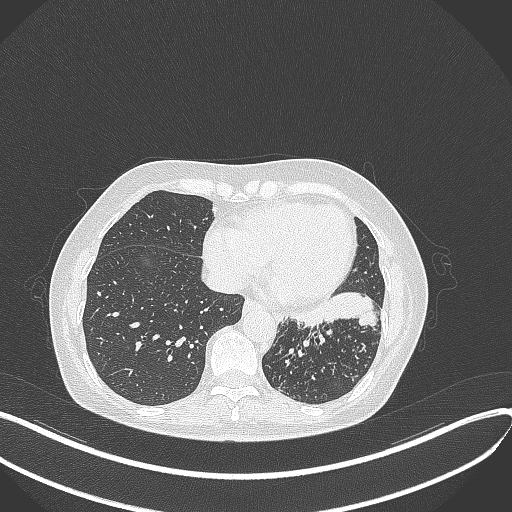
Chest CT, one axial slice. Position 130 of 429 along the scan axis. Reconstruction kernel B70f. 100 kVp. Lung window (W 1500 / L -600 HU). 1 mm slice thickness. 512 × 512 image matrix. Patient: female, 63 years. Case-level facts recorded for this patient, not image findings: clinical TNM (as recorded): T1b N0 M0.
Outlined on this slice (rectangle marked by the reading radiologist):
- lung tumour (recorded histology: adenocarcinoma): bounding box (x1, y1, x2, y2) in pixels: (287, 290, 379, 336)